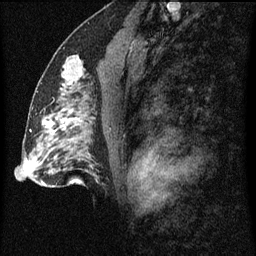
Breast MRI (dynamic contrast-enhanced), one sagittal slice; position 41 of 60 along the scan axis; dynamic contrast-enhanced series, image 2 of 3 at this slice position (ordered by acquisition); 1.5 T; TE 4.2 ms, TR 8 ms; 2 mm slice thickness; 256 × 256 image matrix, field of view 180 × 180 mm. Patient: female, 51 years.
Outlined on this slice (semi-automatic segmentation, software-assisted and operator-edited):
- analysis volume of interest (the breast-tissue region the enhancement analysis was run in; not a lesion): bounding box <54,54,93,103> (left, top, right, bottom; pixels)
- tumour enhancement mask (voxels above the 70 % enhancement threshold inside the analysis volume of interest): <61,82,73,91>